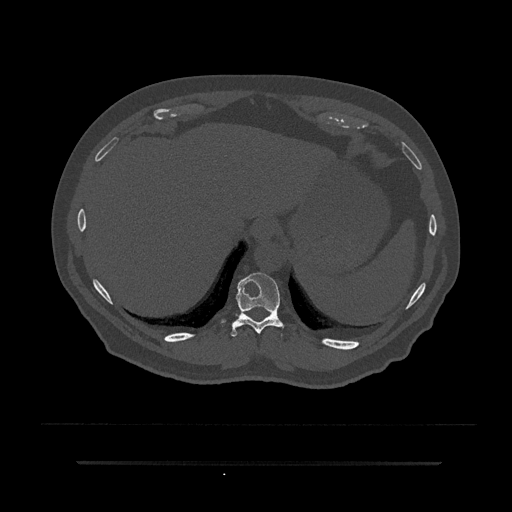
CT including the spine, one axial slice. Position 324 of 797 along the scan axis. Reconstruction kernel Br40s/3. Bone window (W 1800 / L 400 HU). 512 × 512 image matrix, field of view 464 × 464 mm. Male patient, age 59 years. Case-level facts recorded for this patient, not image findings: primary cancer: bile ducts.
Outlined on this slice (semi-automatically segmented with operator editing):
- T10 vertebra: bounding box (x1, y1, x2, y2) in pixels: (221, 273, 284, 337)